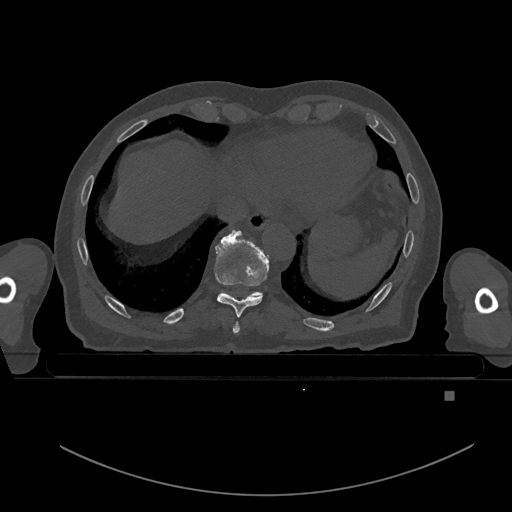
CT including the spine, one axial slice. Position 136 of 969 along the scan axis. Bone window (W 1800 / L 400 HU). 512 × 512 image matrix, field of view 456 × 456 mm. Male patient, age 82 years. From the clinical record (not read from this slice): primary cancer: prostate; vertebrae with lytic lesions (as recorded): T11, T9, T8, T2.
Outlined on this slice (semi-automatically segmented with operator editing):
- T10 vertebra: bounding box (x1, y1, x2, y2) in pixels: (253, 291, 261, 296)
- T8 vertebra: (233, 321, 240, 334)
- T9 vertebra: (214, 230, 269, 317)